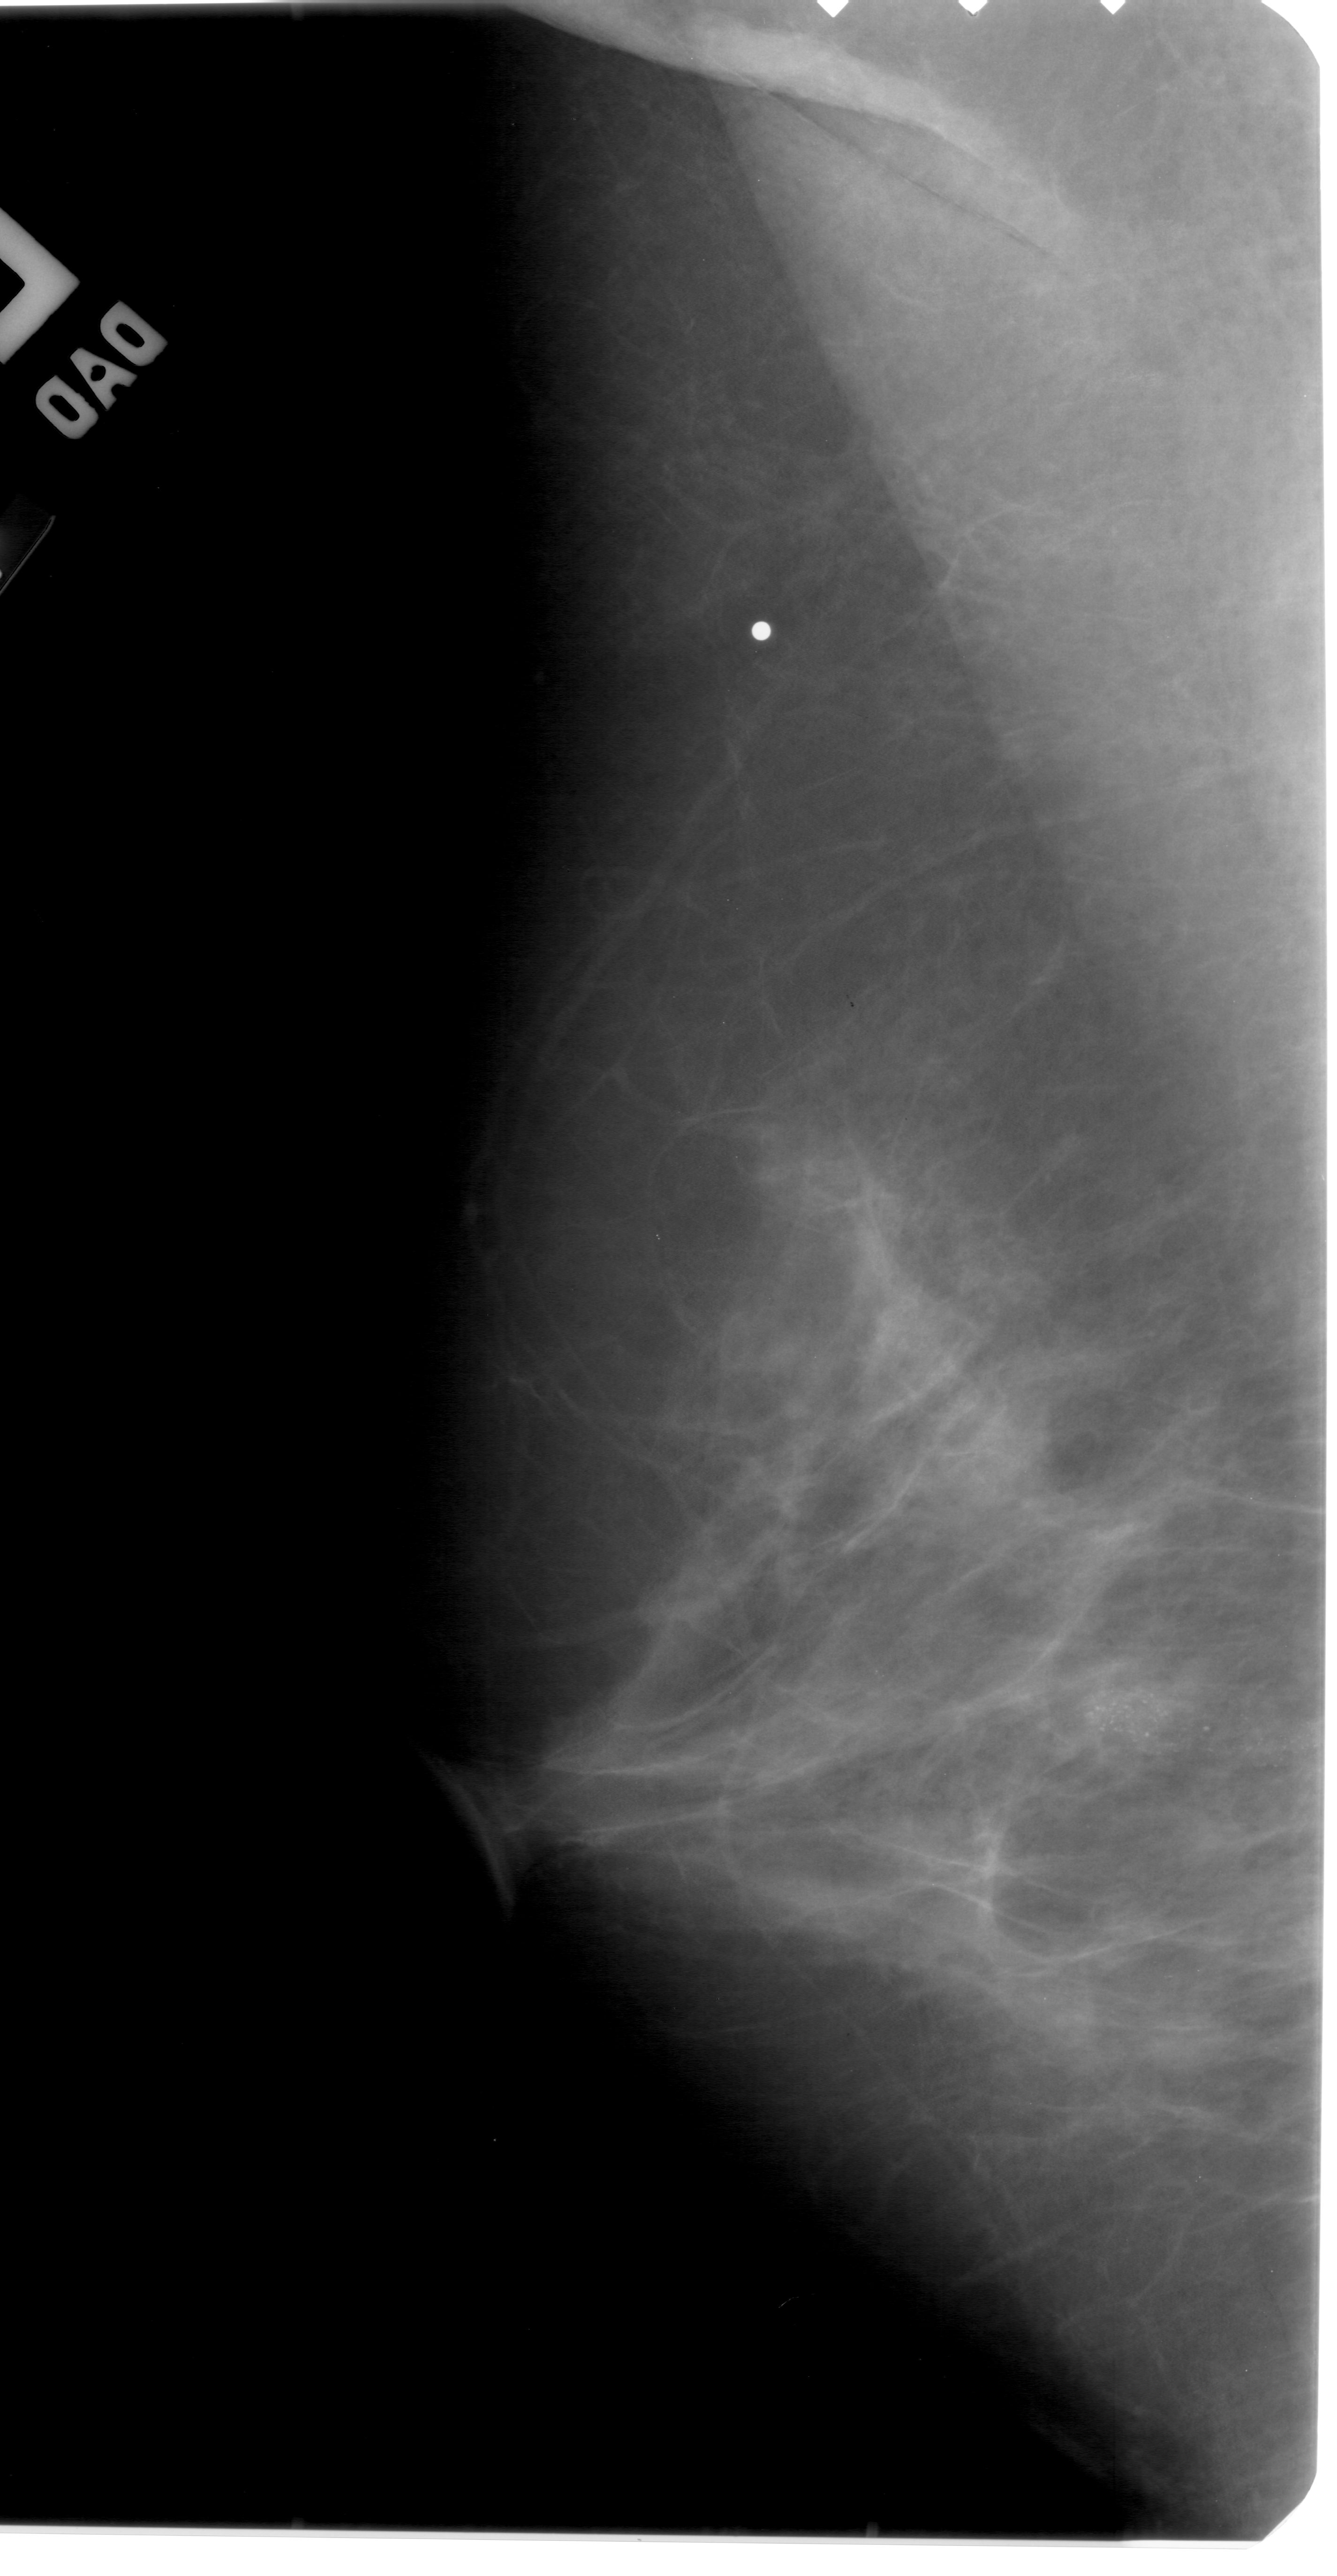
Digitized screen-film mammogram; left breast; MLO view; breast composition: almost entirely fatty (BI-RADS density category 1 of 4).
- Marked findings (only marked abnormalities are described; nothing is implied about the rest of the image): calcifications, morphology pleomorphic, distribution clustered; BI-RADS assessment category 4; pathology result (as recorded, not read from the image): benign.